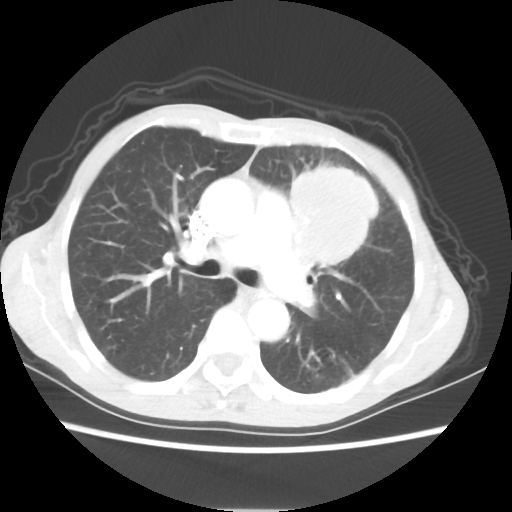
Chest CT, one axial slice. Position 36 of 56 along the scan axis. 80 kVp. Lung window (W 1500 / L -600 HU). 5 mm slice thickness. 512 × 512 image matrix. Female patient, age 60 years. Case-level facts recorded for this patient, not image findings: clinical TNM (as recorded): T4 N1 M0.
Structures marked on this image (rectangle marked by the reading radiologist):
- lung tumour (recorded histology: adenocarcinoma): box from (x=291, y=158) to (x=384, y=277) px